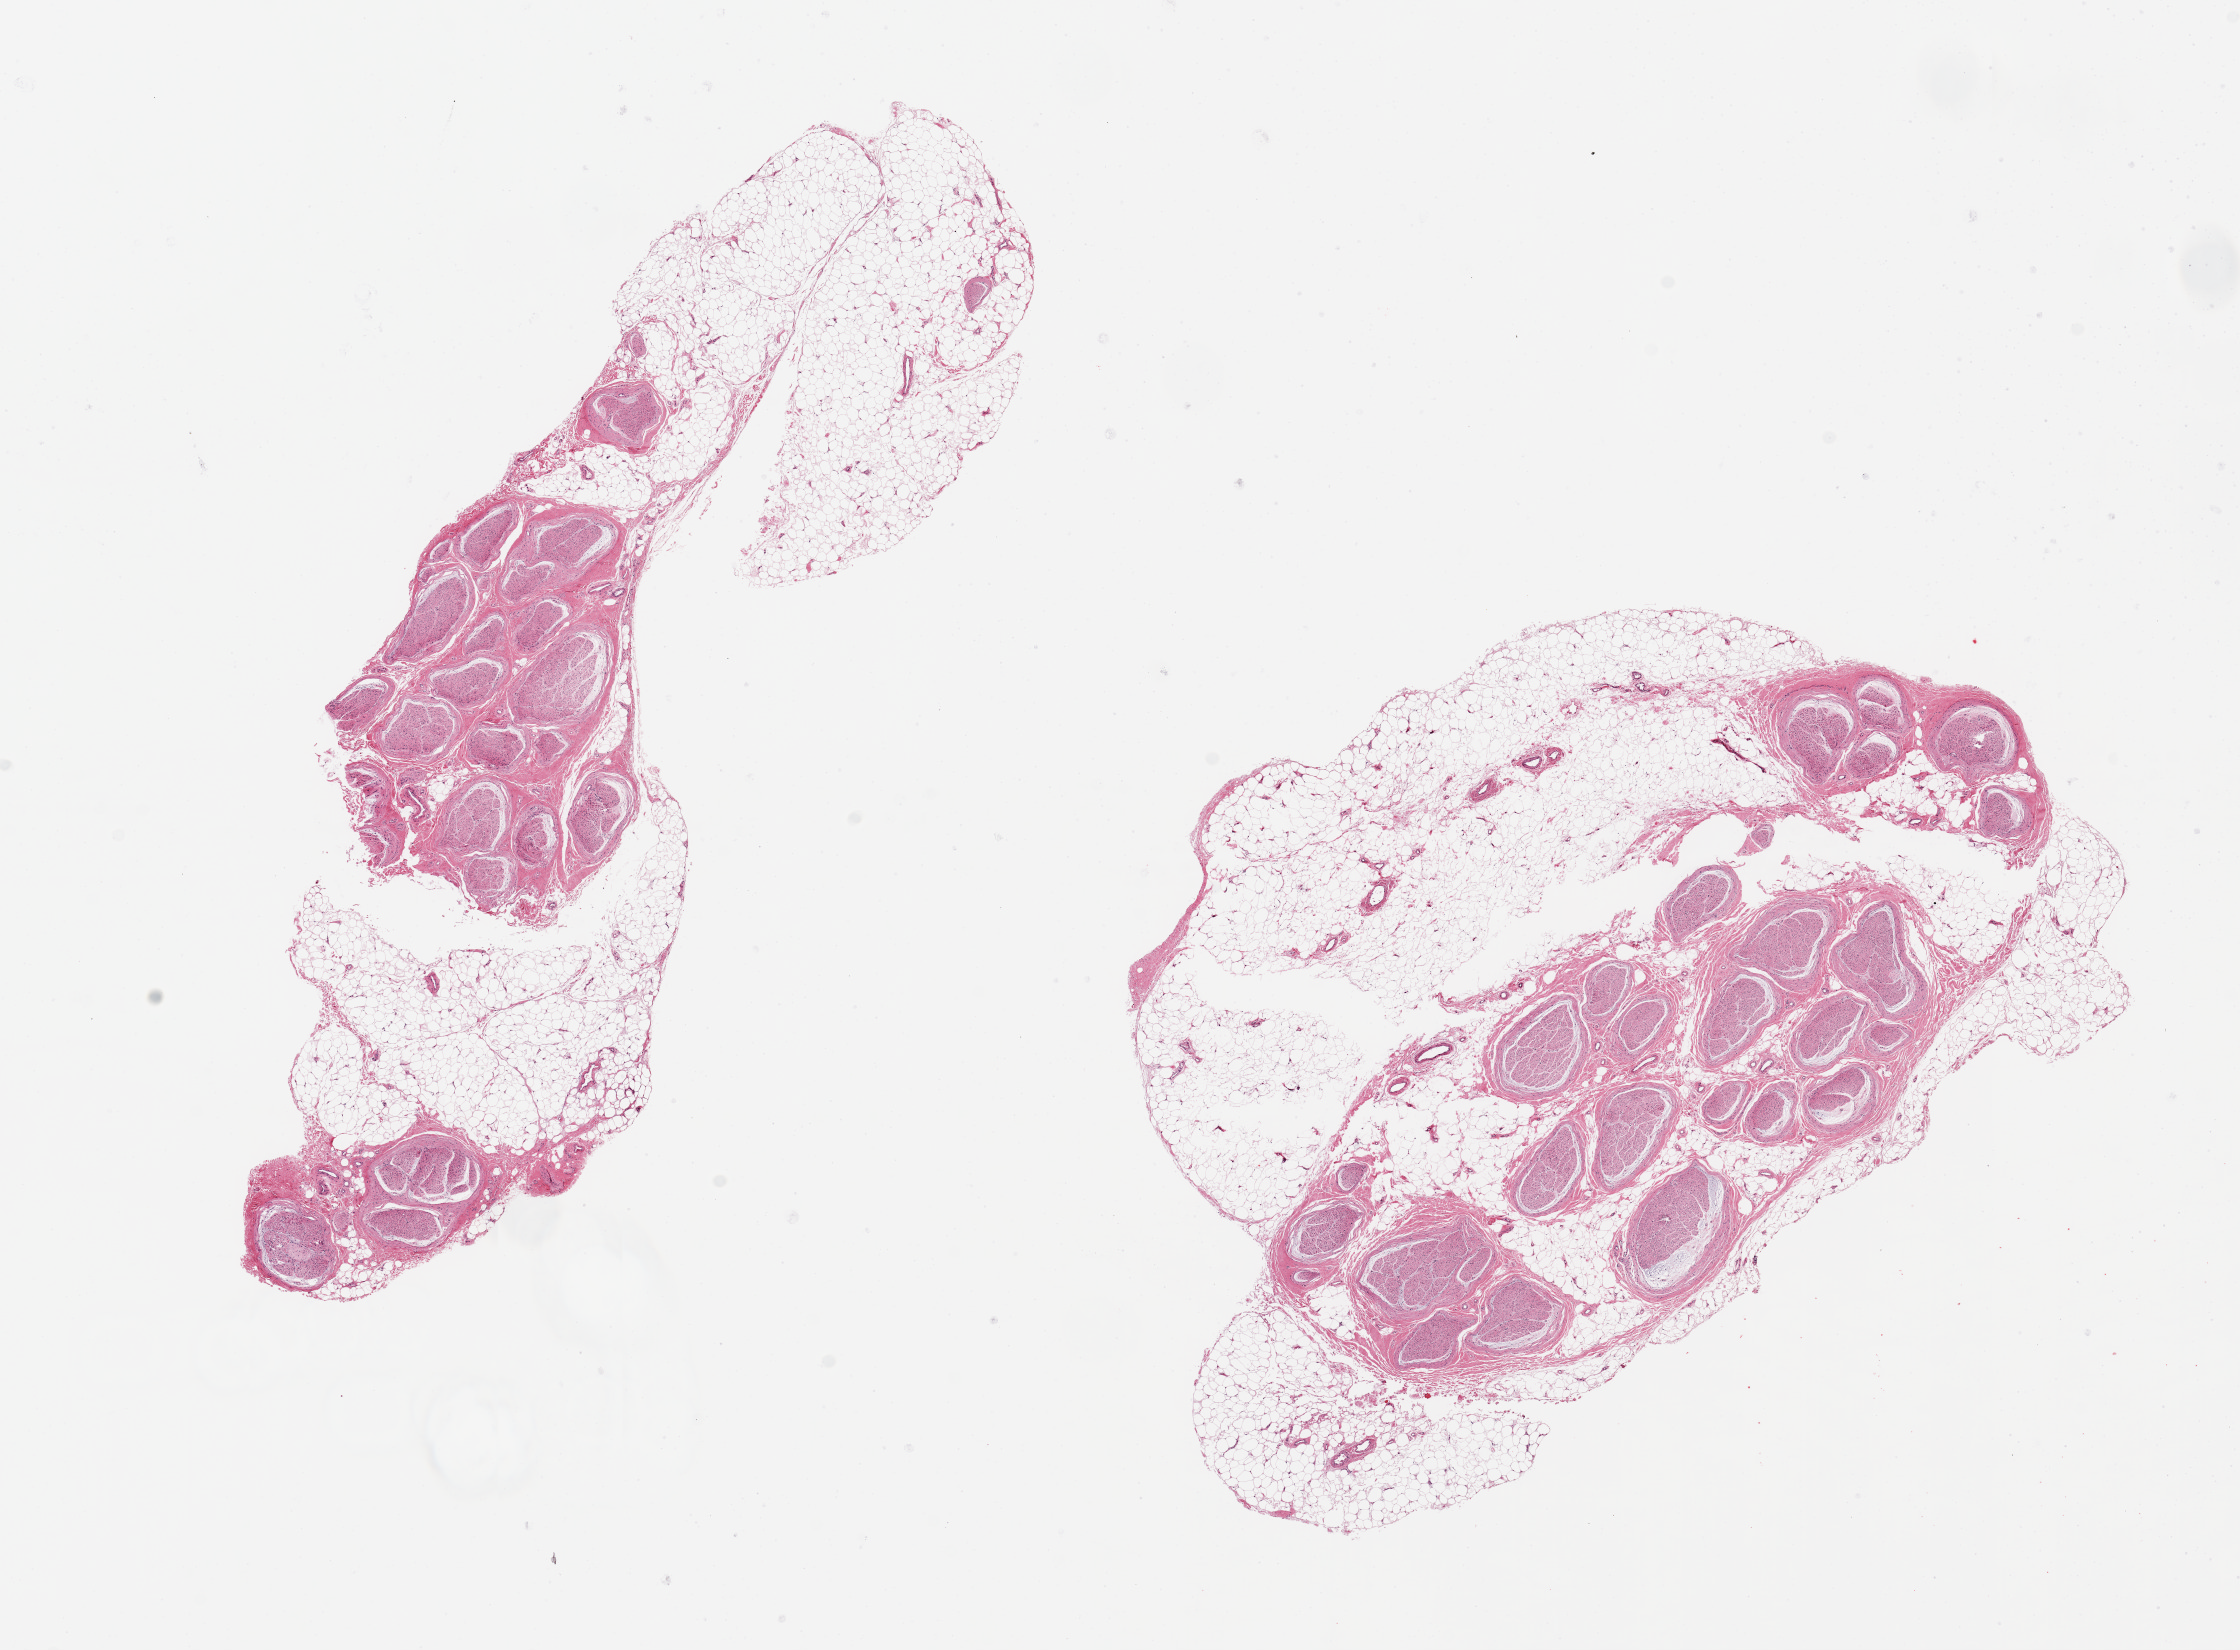
H&E whole-slide image, brightfield — whole scanned area (about 17.7 x 13.1 mm) shown as a low-resolution overview; PAXgene-fixed, paraffin-embedded tissue; sampled site (target tissue): tibial nerve; donor tissue sample. Donor: female.
Review note (as recorded): 2 ~ 6x2.5mm aliquots. 50% or more of both is contaminating peripheral adherent fat.